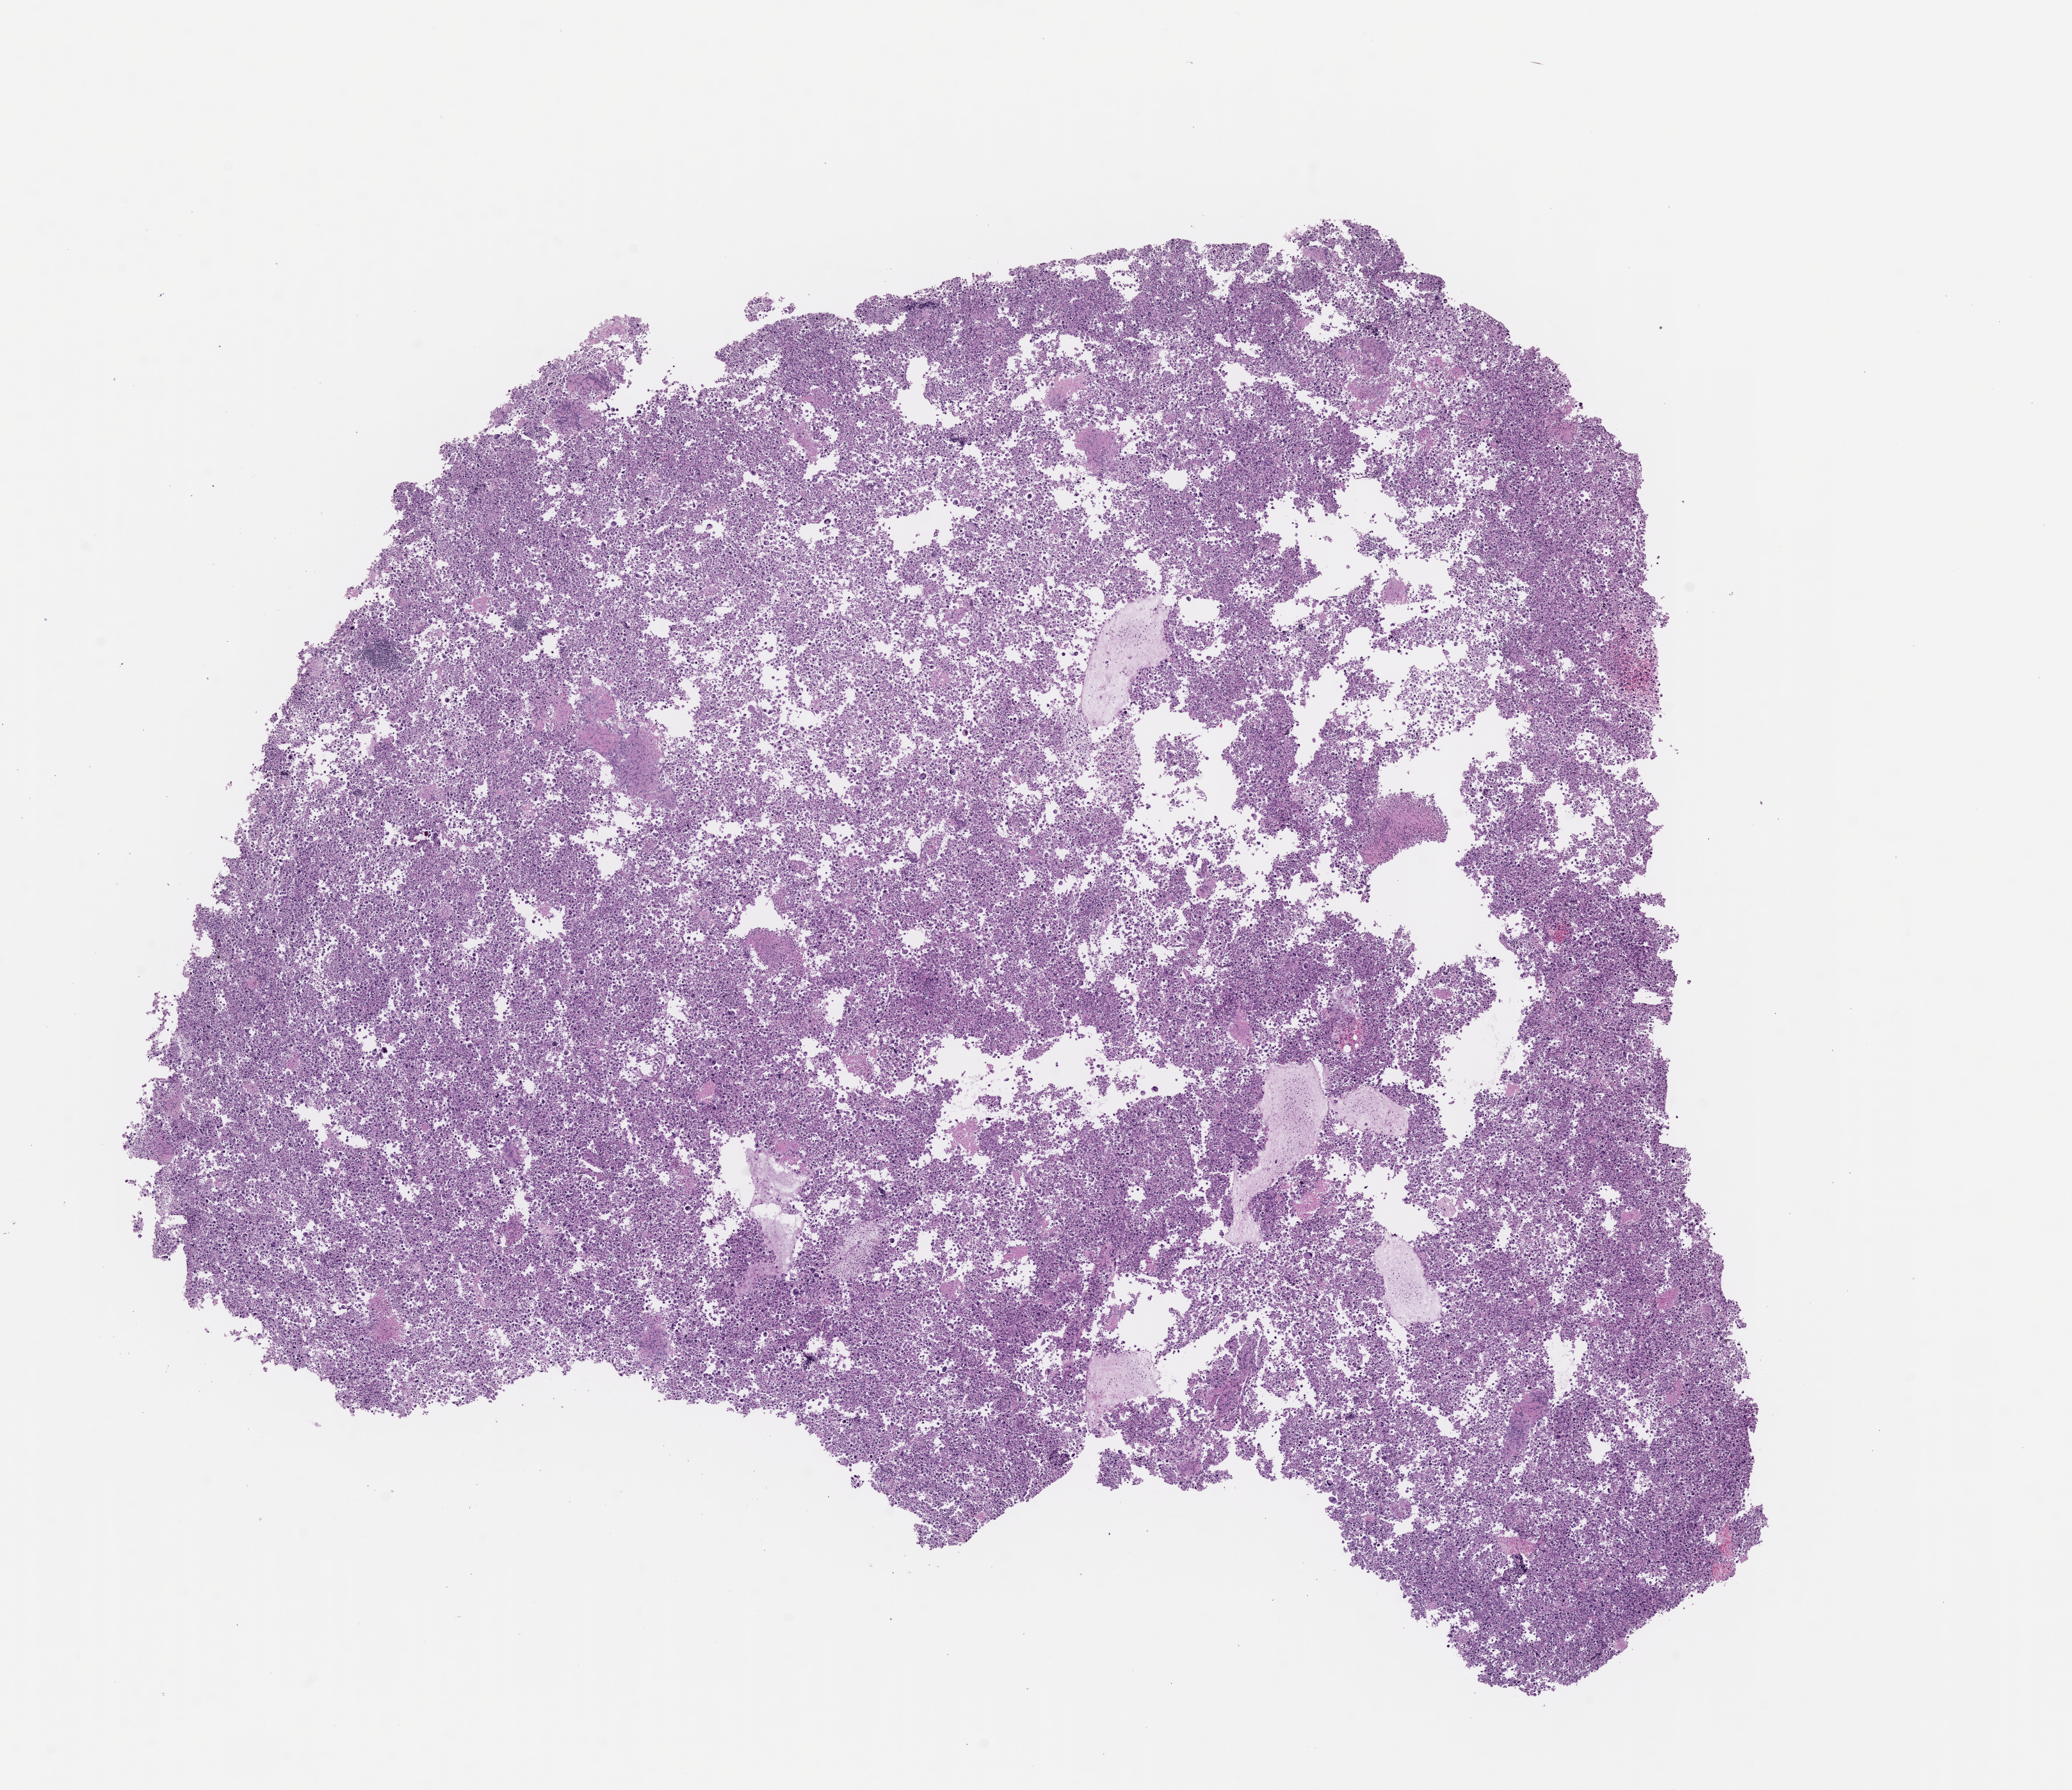
Digitized haematoxylin and eosin-stained section — whole scanned area (about 13.1 x 11.3 mm) shown as a low-resolution overview. FFPE section. Site: lung. Specimen time point: archival tissue. Patient: female.
This section: primary tumor. Diagnosis: Non-Small Cell Lung Carcinoma.